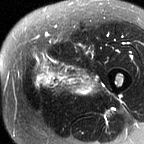
MRI of an extremity soft-tissue mass, one axial slice. Position 19 of 60 along the scan axis. T2-weighted fat-saturated. MR volume resampled by the dataset authors to the PET/CT grid (not the native acquisition matrix). 3.27 mm slice thickness. 144 × 144 image matrix, field of view 141 × 141 mm. Female patient. From the clinical record (not read from this slice): histological type: pleiomorphic leiomyosarcoma; grade: intermediate; site of the primary tumour: left thigh.
Structures marked on this image (expert contour drawn on MRI and transferred to this co-registered scan by the dataset authors):
- gross tumour volume including surrounding oedema: bounding box <32,54,101,96> (left, top, right, bottom; pixels)